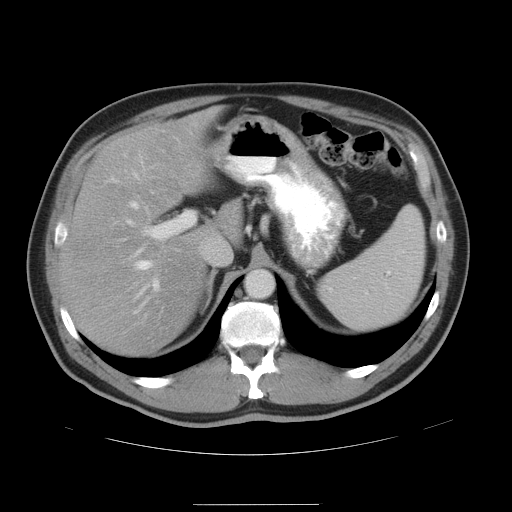
Contrast-enhanced abdominal CT, one axial slice; slice 32 of 47 in the series (ordered by position); 120 kVp; soft-tissue window (W 400 / L 40 HU); 5 mm slice thickness; 512 × 512 image matrix, field of view 420 × 420 mm. Male patient, age 61 years. From the clinical record (not read from this slice): diagnosis: colorectal cancer liver metastases, imaged before liver resection; multiple liver metastases: no; largest metastasis: 1.2 cm; disease in both lobes: no.
Annotated regions visible in this slice (expert manual segmentation):
- hepatic veins: box from (x=113, y=174) to (x=156, y=295) px
- liver: (x=64, y=106)–(x=240, y=358)
- planned liver remnant (the part of the liver to remain after resection): (x=64, y=106)–(x=241, y=358)
- portal vein (with intrahepatic branches): (x=129, y=211)–(x=196, y=314)